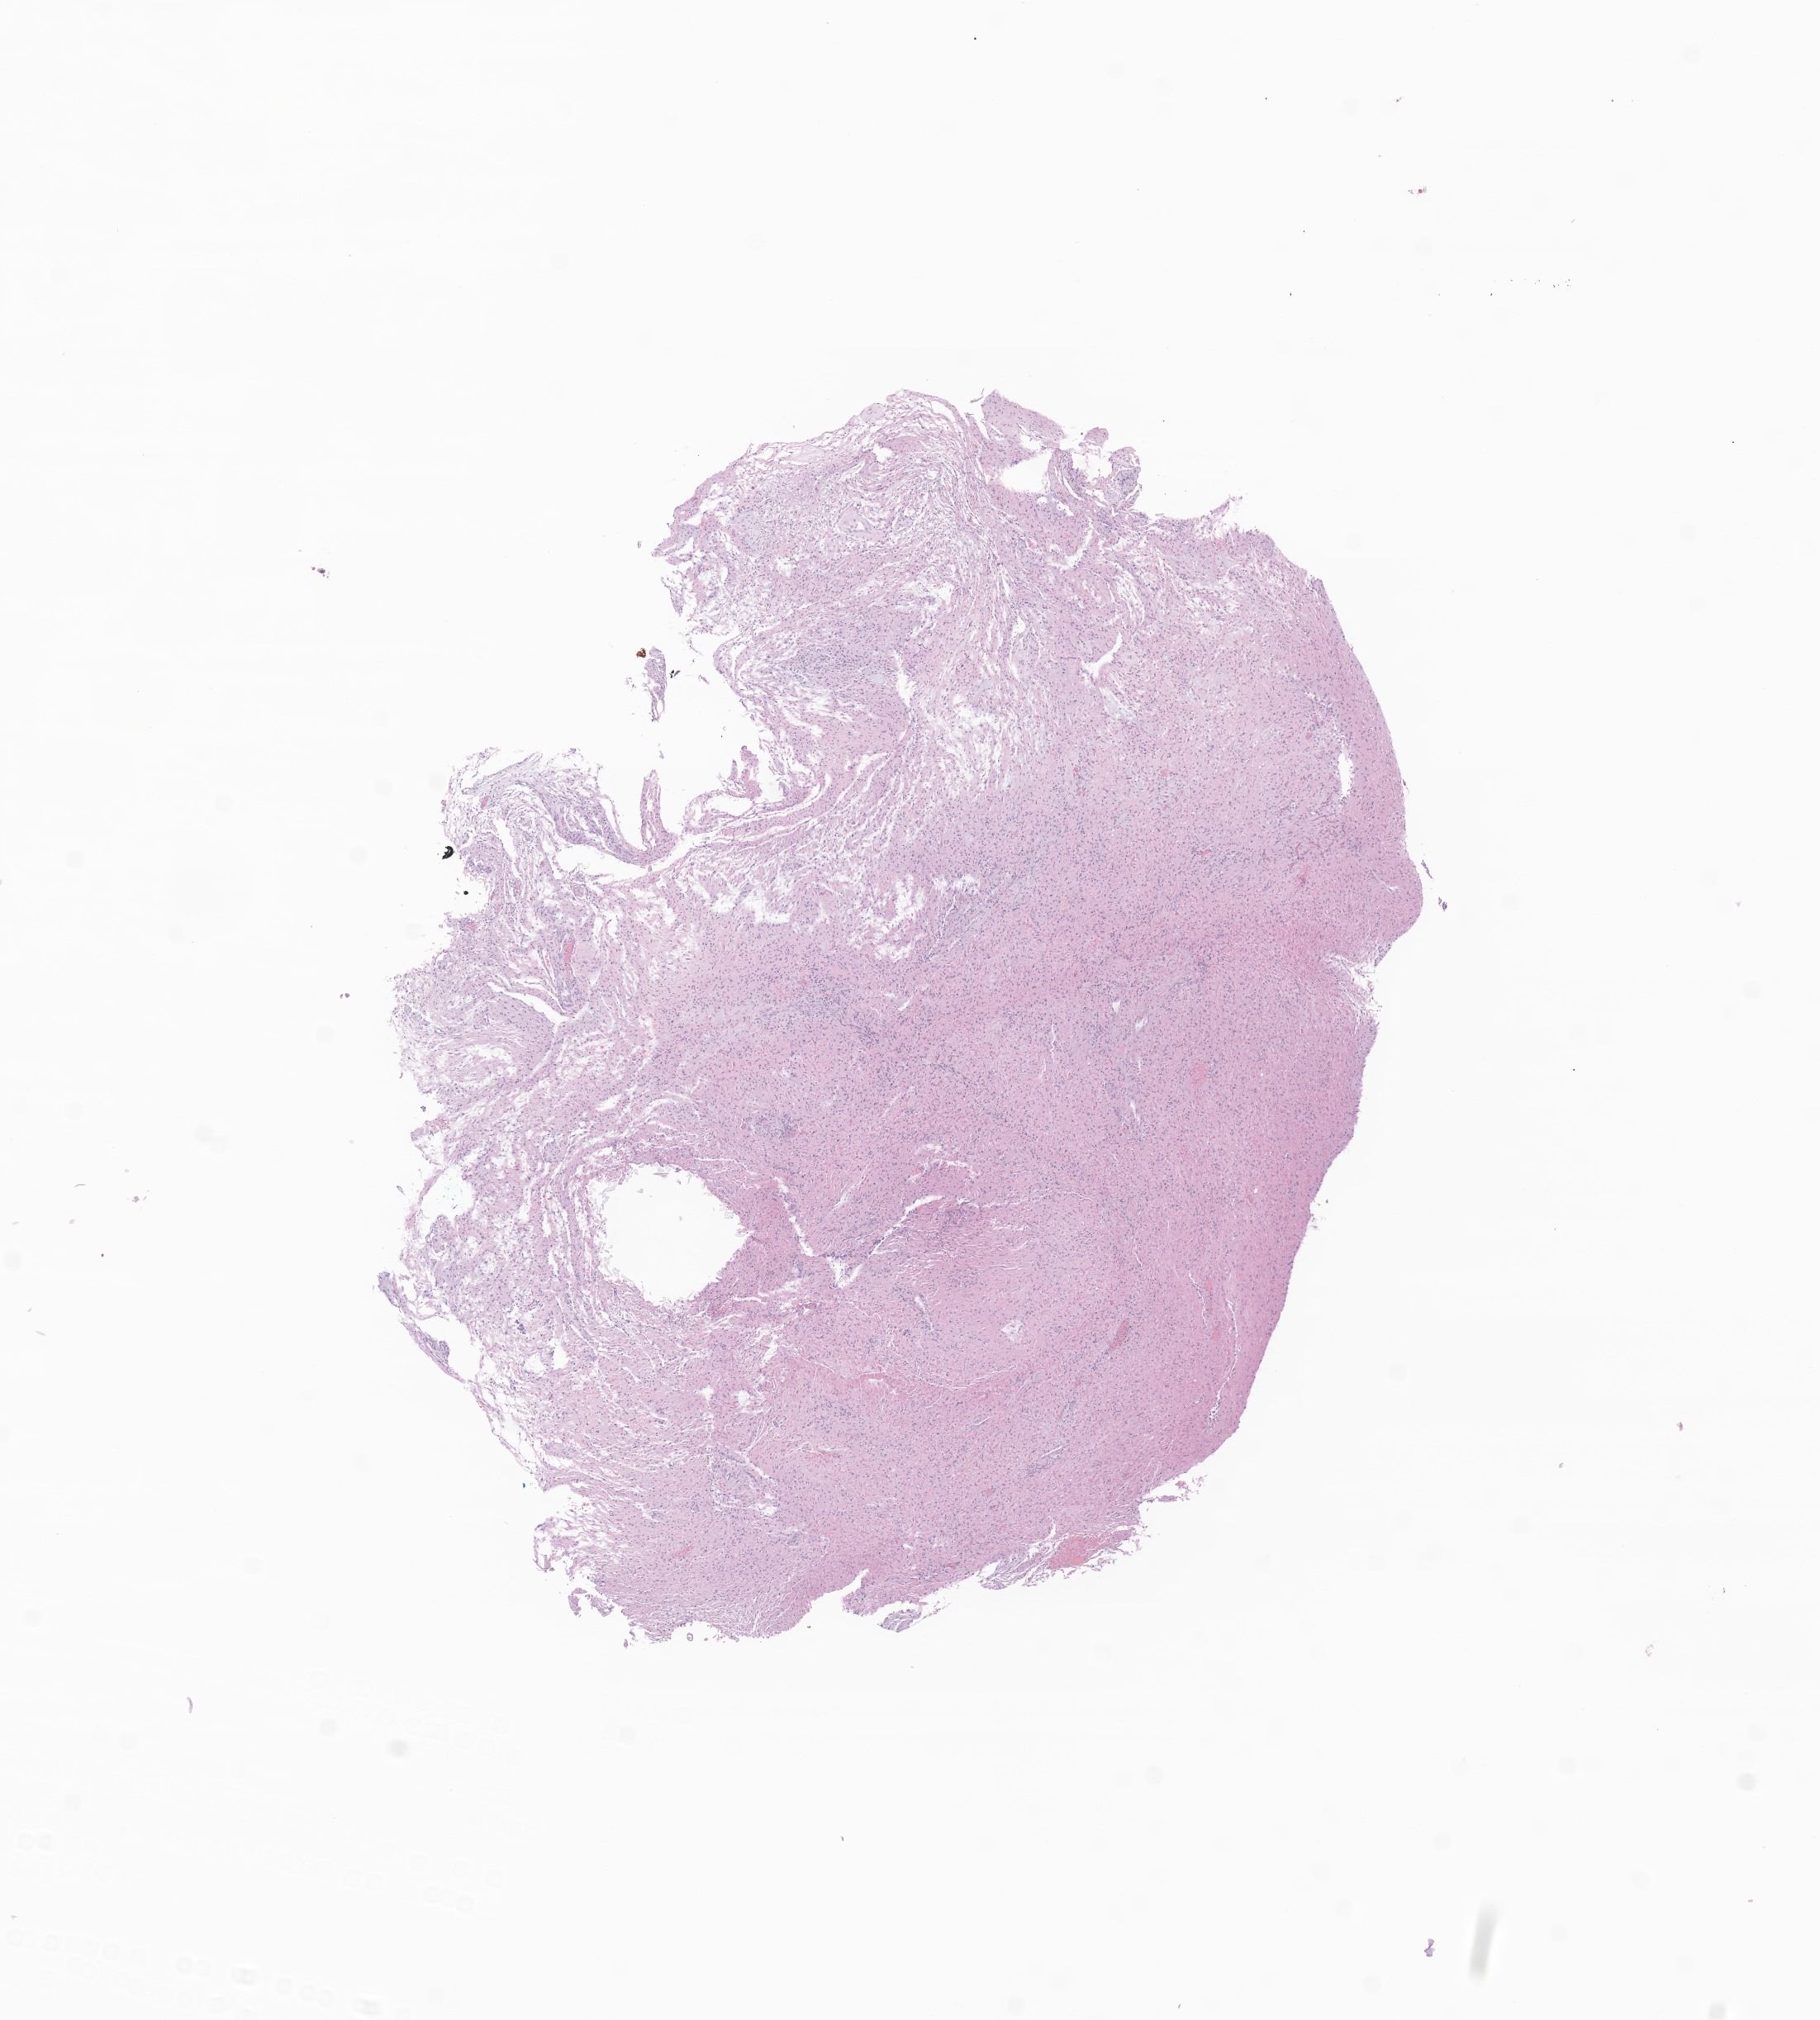
Hematoxylin and eosin (H&E) whole-slide image of tumor tissue from the brain — whole scanned area (about 9.3 x 10.3 mm) shown as a low-resolution overview. Formalin-fixed paraffin-embedded section. Patient: male, age 115 months (9 years 7 months).
- recorded diagnosis: Pilocytic astrocytoma